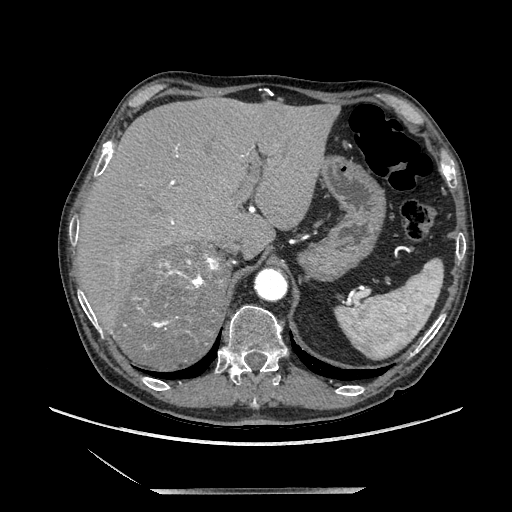
Contrast-enhanced abdominal CT, one axial slice. Slice 159 of 243 in the series (ordered by position). Soft-tissue window (W 400 / L 40 HU). 1.25 mm slice thickness. 512 × 512 image matrix, field of view 420 × 420 mm. Male patient. From the clinical record (not read from this slice): diagnosis: adrenocortical carcinoma; tumour side: right adrenal; tumour size at pathology: 16 cm; Ki-67 index: 17 %; stage (as recorded): 3.
Structures marked on this image (semi-automatic segmentation, software-assisted and operator-edited):
- mass: box from (x=117, y=245) to (x=231, y=369) px